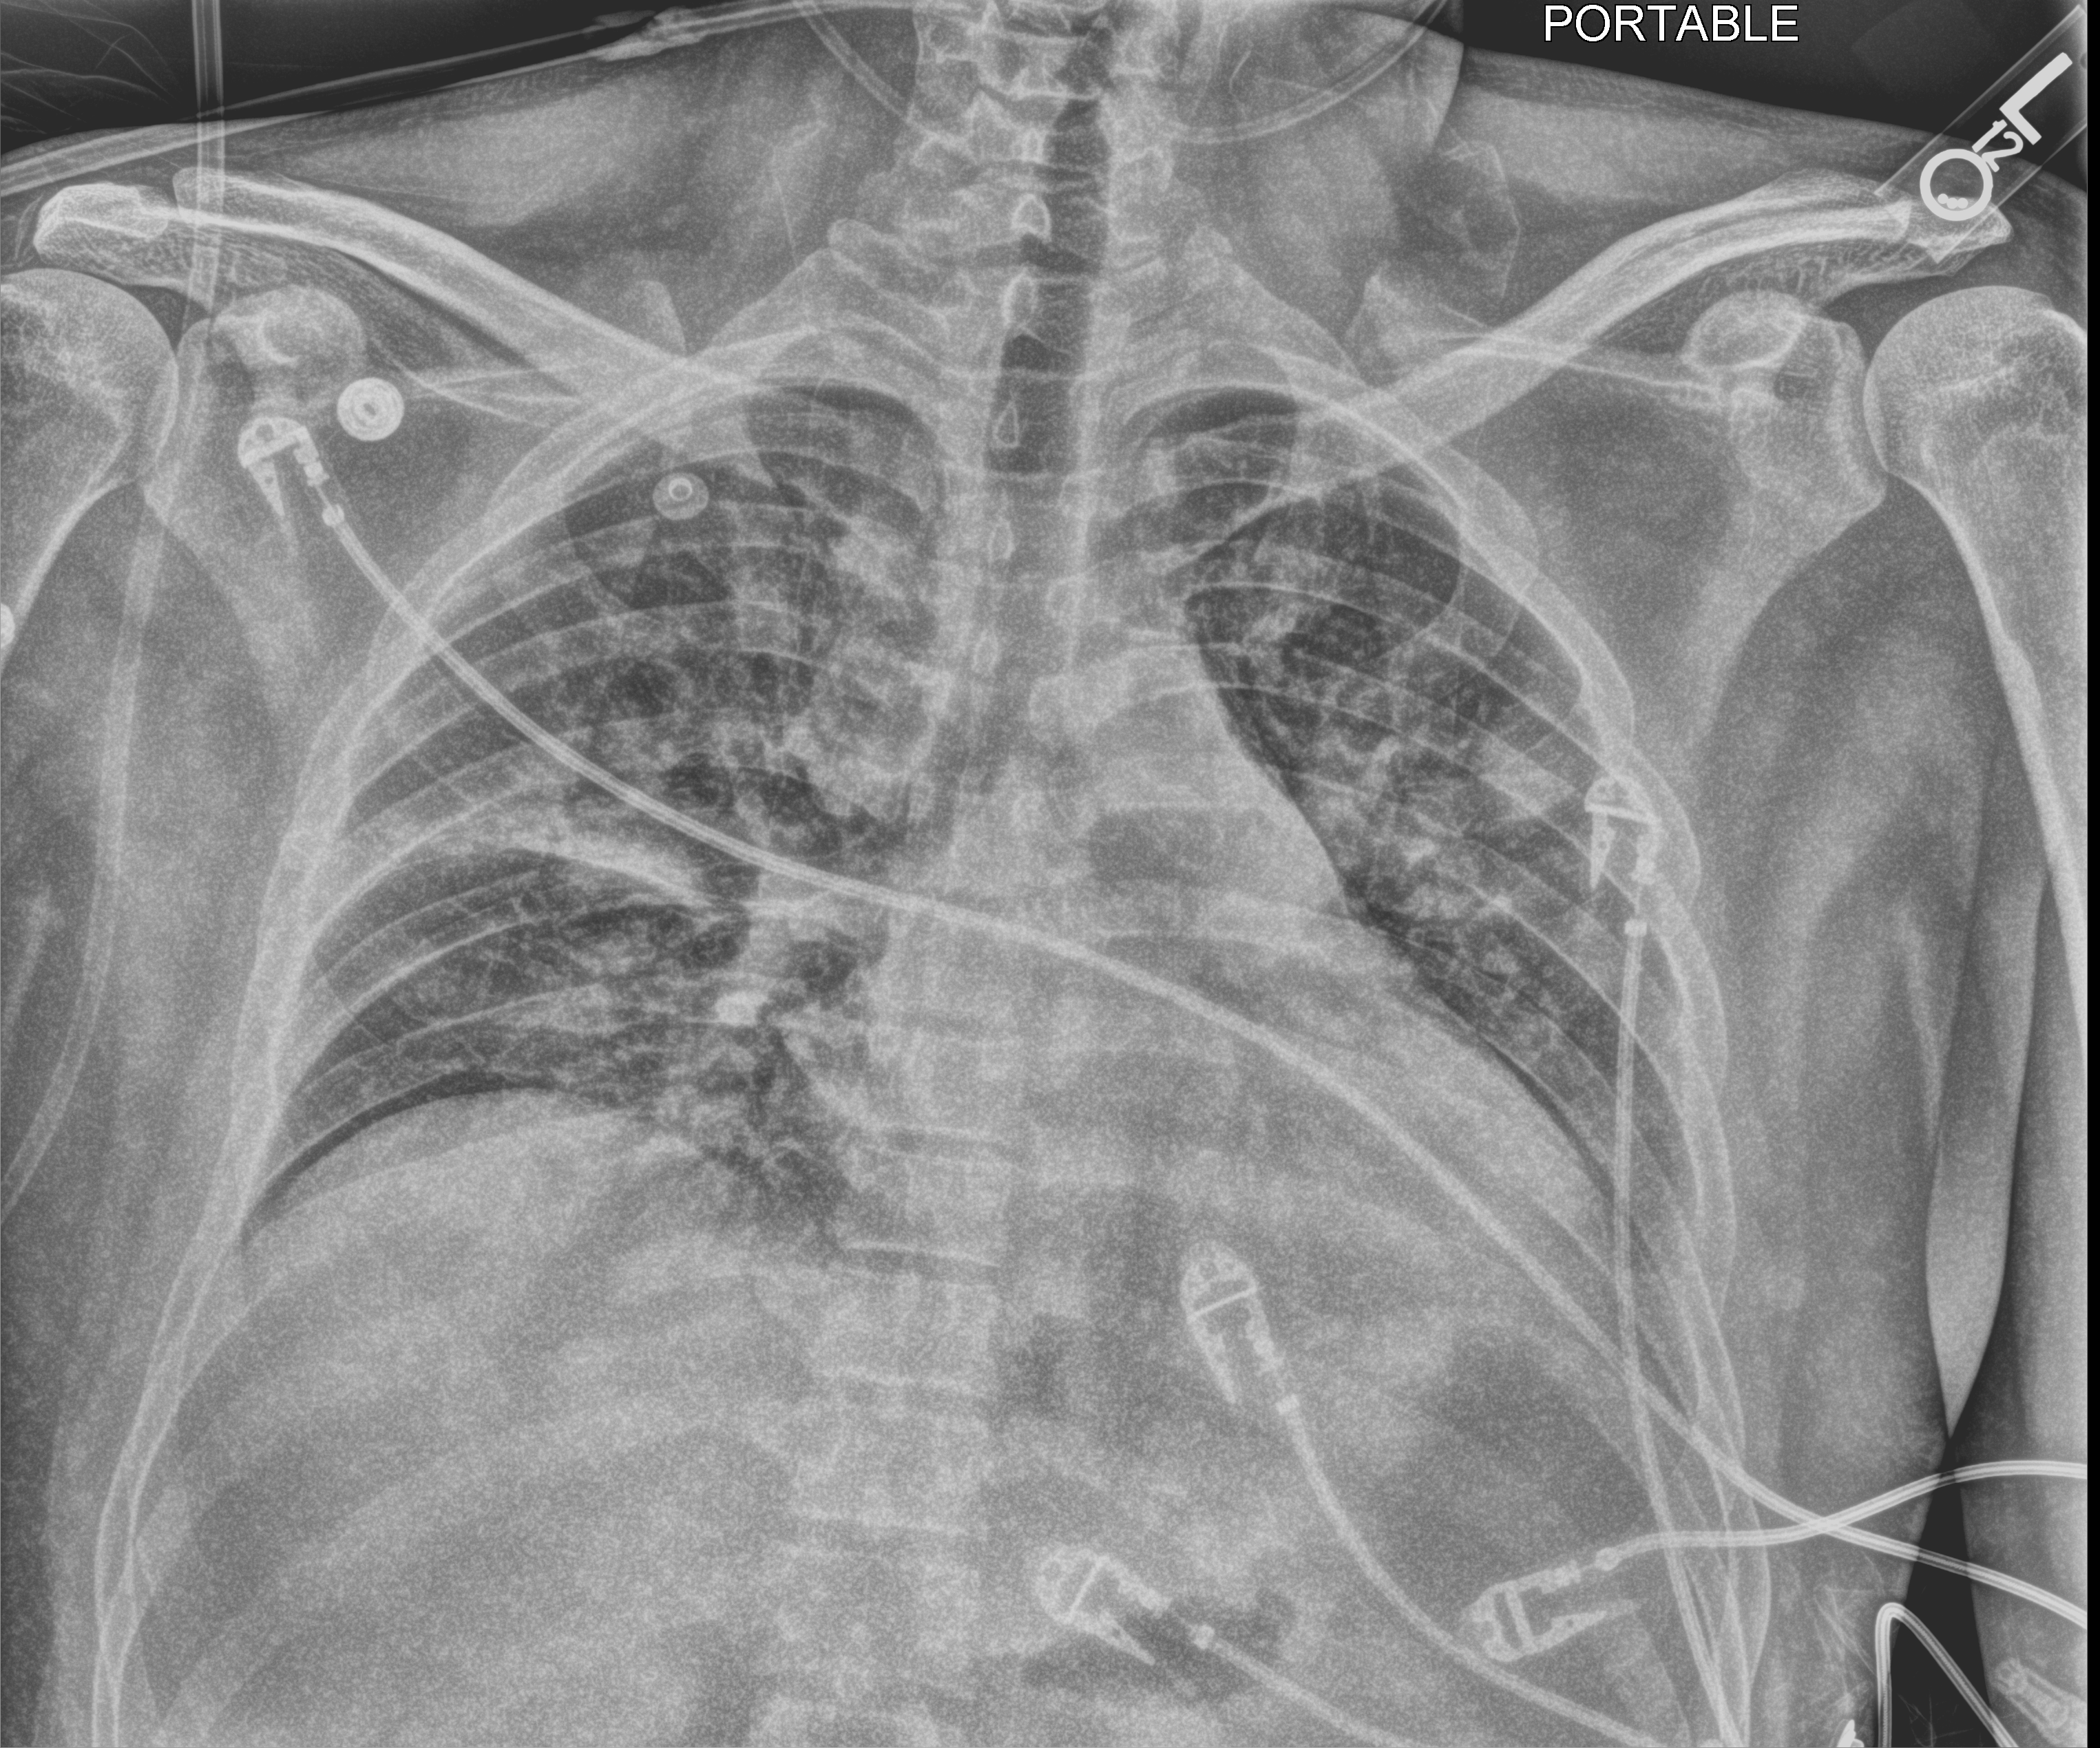
Portable chest radiograph; anteroposterior (AP) projection. Patient hospitalised with COVID-19, aged 18–59 years.
Hospital-stay facts (about this admission, not read from this image; timing relative to this image not recorded):
- COPD (admission record): no